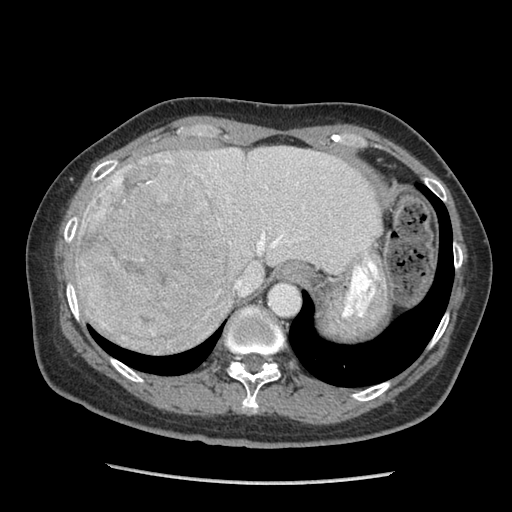
Contrast-enhanced abdominal CT (liver protocol), one axial slice; position 71 of 105 along the scan axis; reconstruction kernel STANDARD; soft-tissue window (W 400 / L 40 HU); 2.5 mm slice thickness; 512 × 512 image matrix, field of view 340 × 340 mm. From the clinical record (not read from this slice): diagnosis: hepatocellular carcinoma (patient treated with transarterial chemoembolisation; whether this scan precedes or follows treatment is not stated here); TNM stage (as recorded): Stage-I; Child-Pugh class: A; tumour differentiation: moderately differentiated; tumour size: 11.1 cm.
Structures marked on this image (semi-automatically segmented with operator editing):
- abdominal aorta: box from (x=269, y=283) to (x=300, y=316) px
- liver parenchyma outside the tumour (the mass and vessels are separate outlines, so this box may not span the whole liver): (x=74, y=146)–(x=382, y=334)
- mass: (x=75, y=155)–(x=229, y=353)
- liver vessels: (x=257, y=183)–(x=298, y=254)